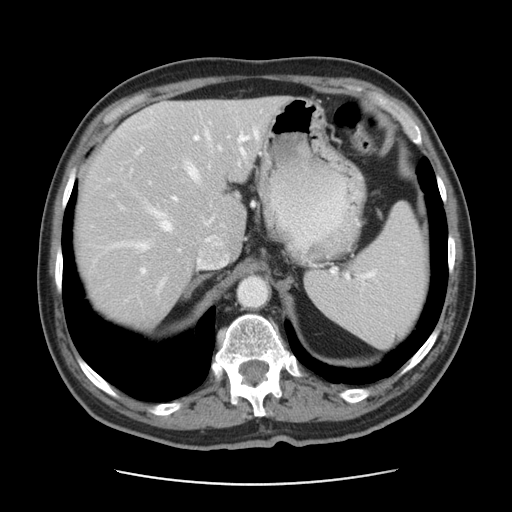
Contrast-enhanced abdominal CT, one axial slice; 120 kVp; intravenous contrast given; soft-tissue window (W 400 / L 40 HU); 5 mm slice thickness; 512 × 512 image matrix. Male patient, age 73 years. From the clinical record (not read from this slice): diagnosis: colorectal cancer liver metastases, imaged before liver resection; multiple liver metastases: yes; largest metastasis: 0.5 cm; chemotherapy before resection: yes.
Annotated regions visible in this slice (manually delineated by an expert):
- hepatic veins: bounding box [x1, y1, x2, y2] px = [113, 130, 258, 295]
- liver: [77, 97, 282, 325]
- planned liver remnant (the part of the liver to remain after resection): [117, 97, 283, 253]
- portal vein (with intrahepatic branches): [140, 132, 250, 275]